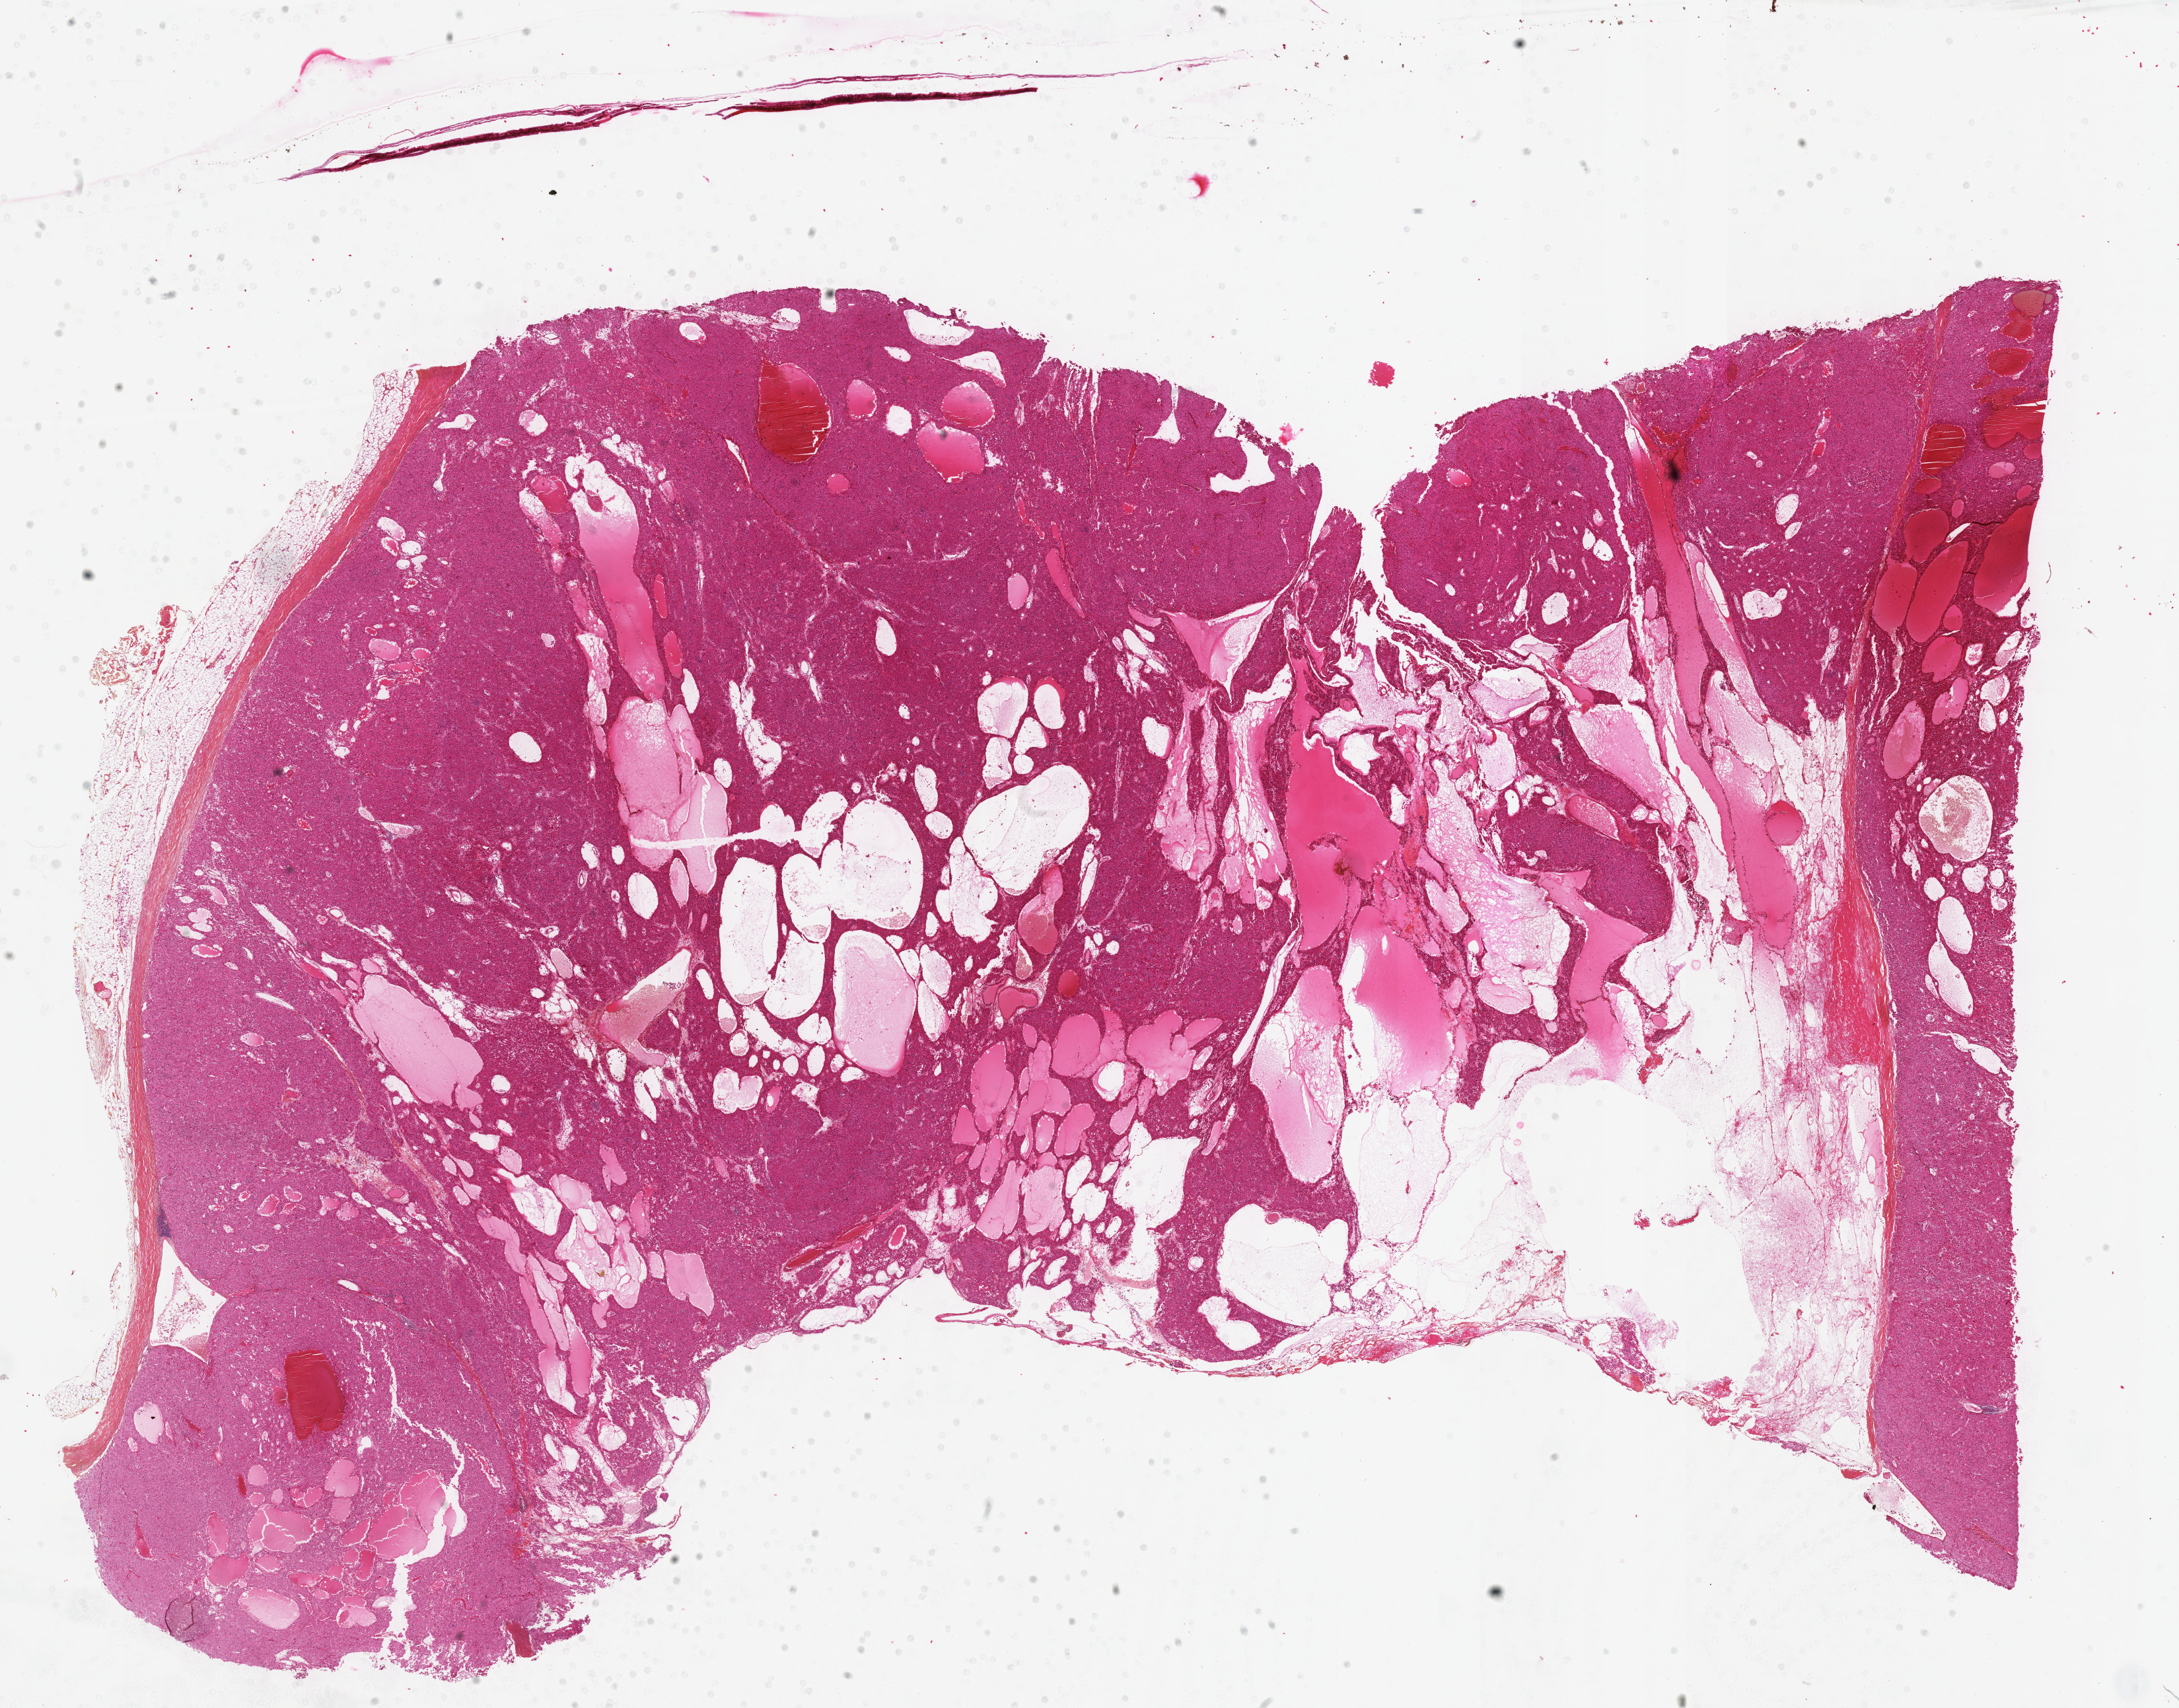
Whole-slide histology image, Hematoxylin and eosin (H&E) stained — low-resolution overview of the scanned area, about 26.7 x 20.9 mm (slide scanned at 40x); formalin-fixed paraffin-embedded (FFPE) diagnostic section; primary tumour sample from the adrenal cortex. Patient: male, age at initial diagnosis 62 years.
* diagnosis: Adrenal cortical carcinoma (cortex of adrenal gland)